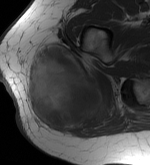
MRI of an extremity soft-tissue mass, one axial slice; slice 22 of 56 in the series (ordered by position); MR volume resampled by the dataset authors to the PET/CT grid (not the native acquisition matrix); 3.27 mm slice thickness; 150 × 165 image matrix. Female patient. Case-level facts recorded for this patient, not image findings: histological type: epithelioid sarcoma with vascular differentiation; site of the primary tumour: right buttock.
Annotated regions visible in this slice (expert contour drawn on MRI and transferred to this co-registered scan by the dataset authors):
- gross tumour volume (mass): bounding box [x1, y1, x2, y2] px = [25, 42, 111, 135]